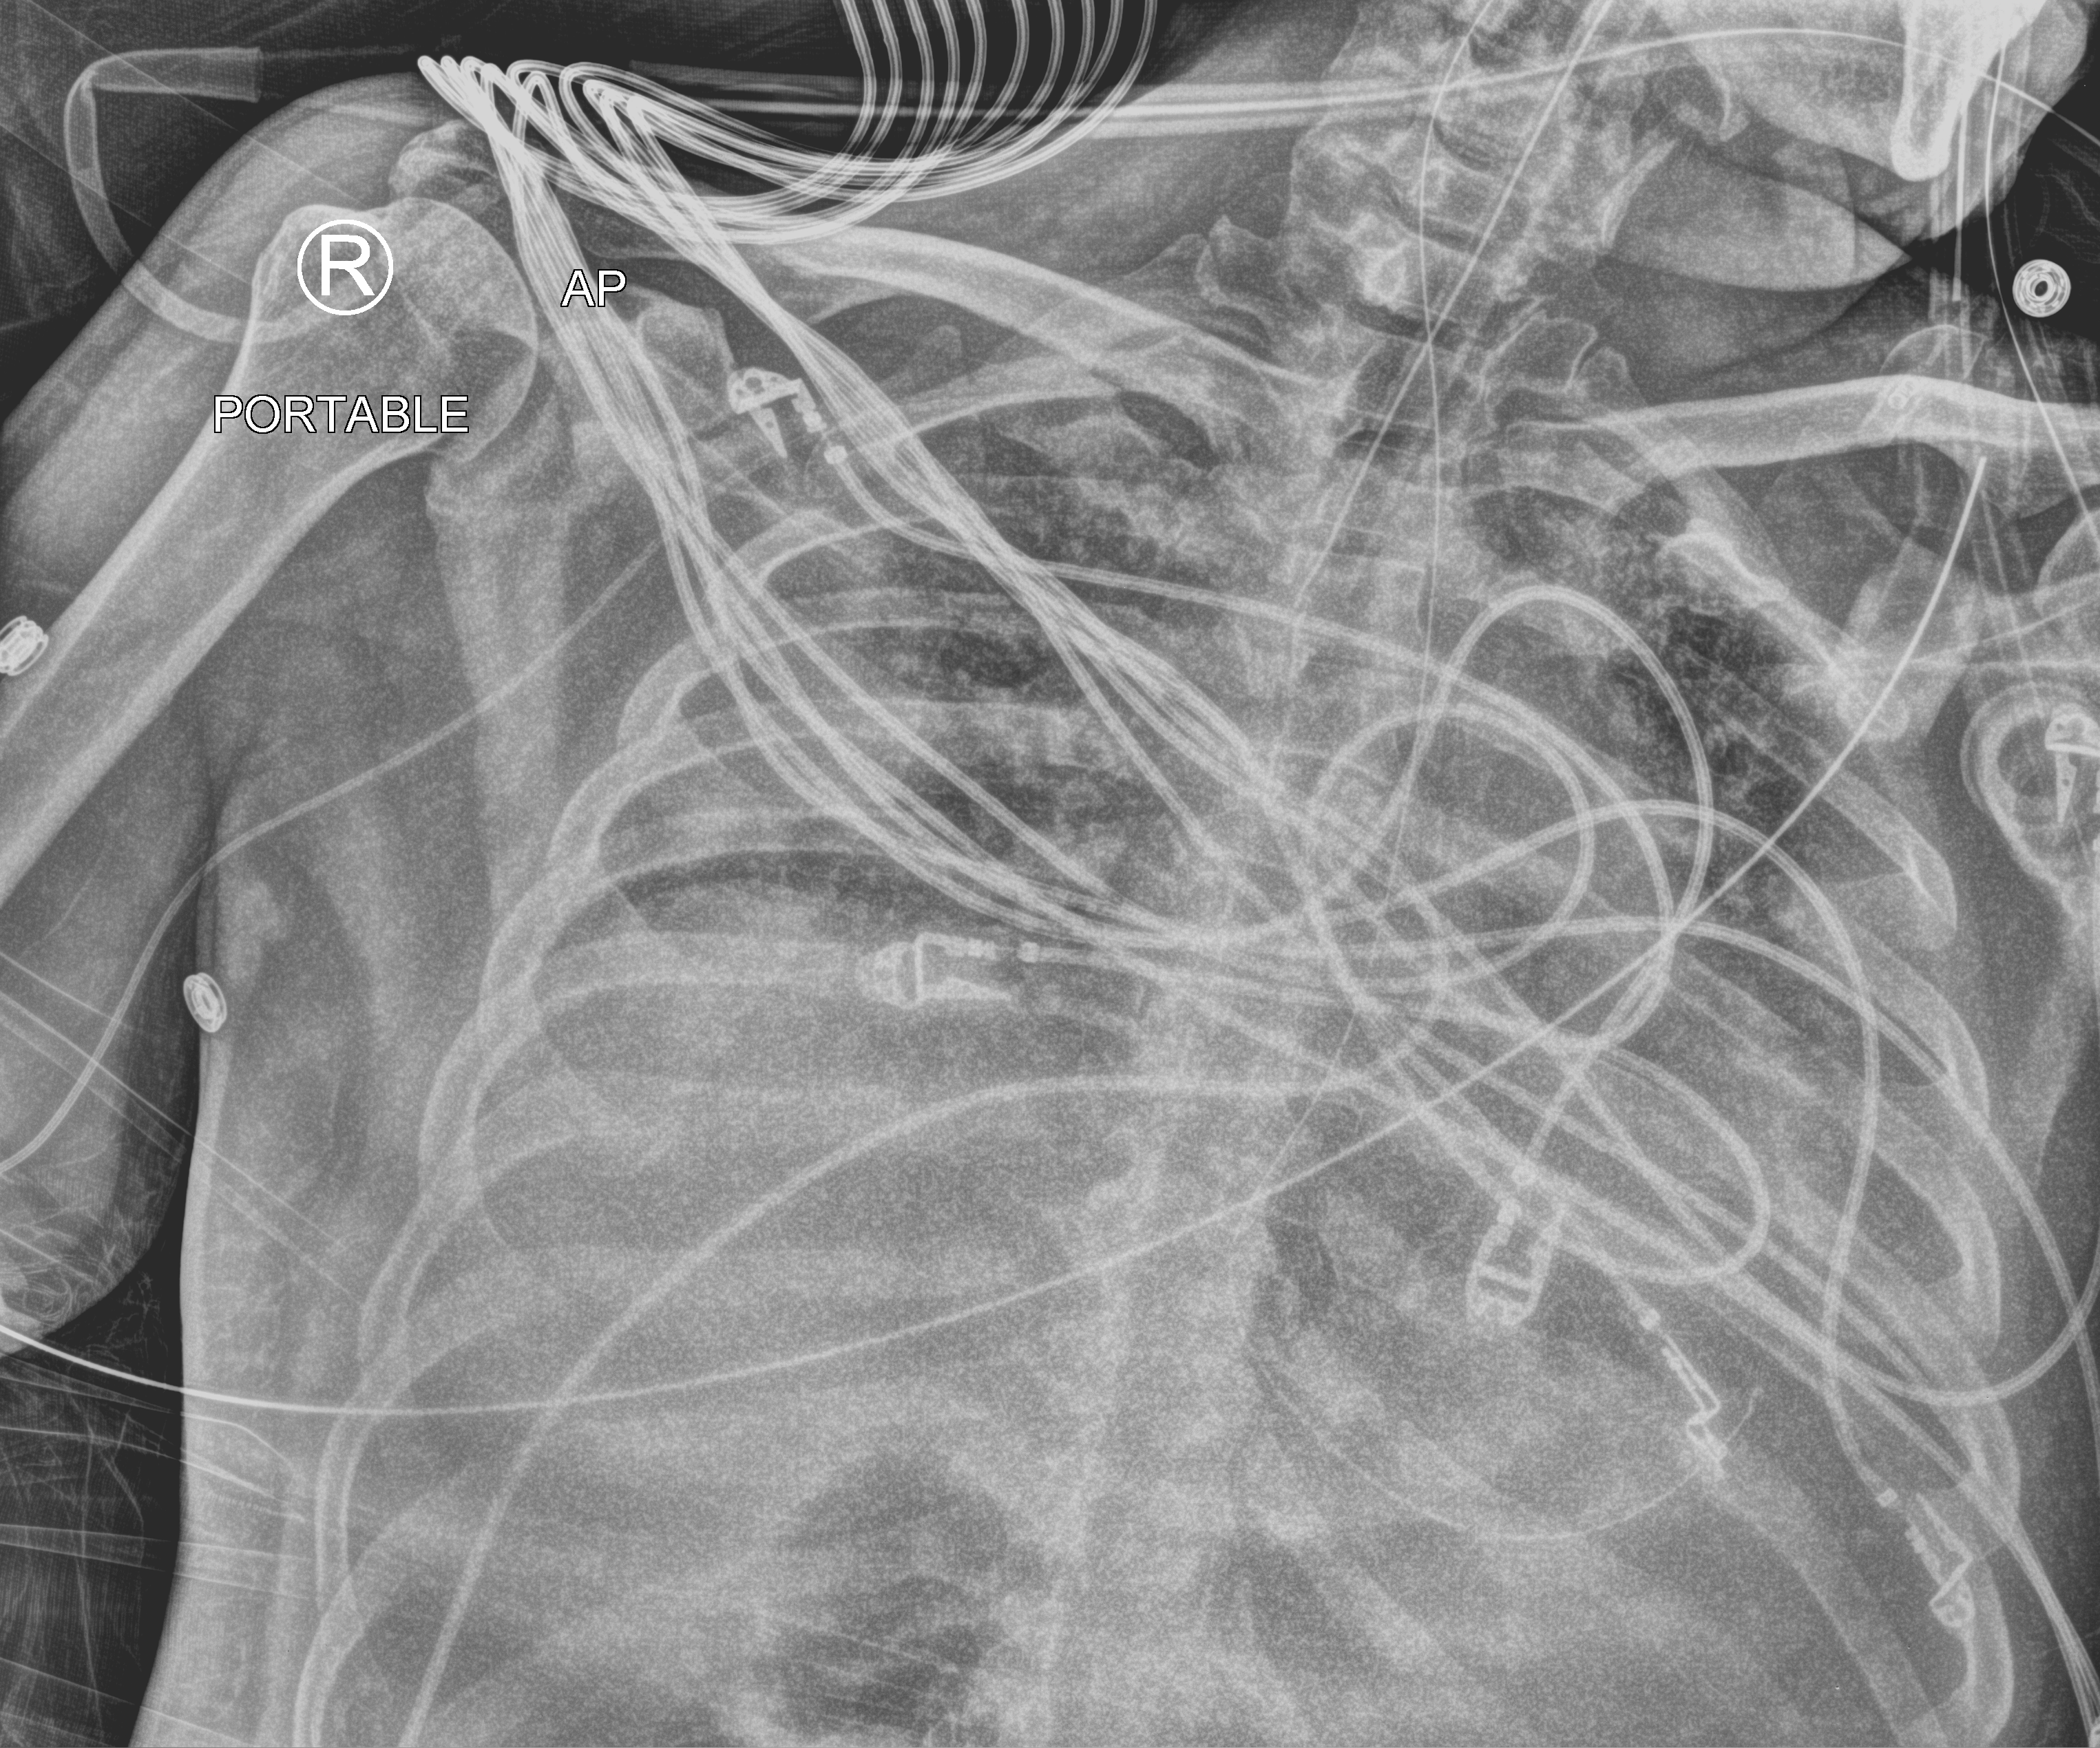
Bedside chest radiograph (computed radiography); anteroposterior (AP) projection. Male patient hospitalised with COVID-19, age 60–74 years.
Hospital-stay facts (about this admission, not read from this image; timing relative to this image not recorded): mechanically ventilated during this hospital stay: yes; hypertension (admission record): no.